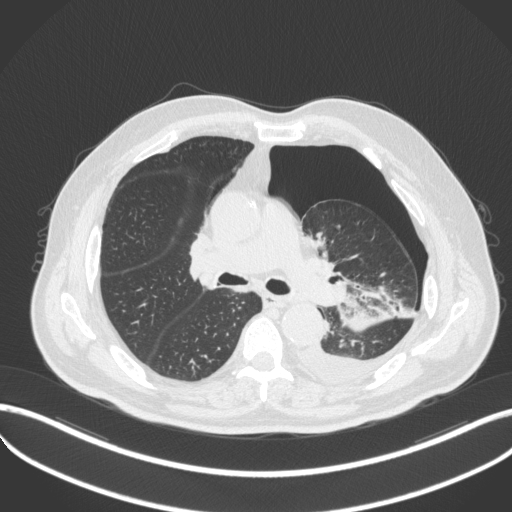
Chest CT, one axial slice. Position 312 of 466 along the scan axis. Lung window (W 1500 / L -600 HU). 1 mm slice thickness. 512 × 512 image matrix. Patient: male, 76 years. Case-level facts recorded for this patient, not image findings: clinical TNM (as recorded): T3 N0 M1b.
Structures marked on this image (bounding box drawn by a radiologist):
- lung tumour (recorded histology: adenocarcinoma): bounding box (x1, y1, x2, y2) in pixels: (333, 278, 394, 332)